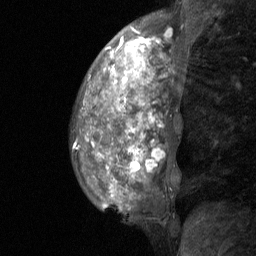
Breast MRI (dynamic contrast-enhanced), one sagittal slice. Slice 22 of 64 in the series (ordered by position). Dynamic contrast-enhanced study with each time point stored as its own series, time point 2 of 3 at this slice position (early post-contrast, ordered by acquisition time). 1.5 T. TE 4.8 ms, TR 27 ms. 256 × 256 image matrix, field of view 180 × 180 mm. Female patient, age 36 years. From the clinical record (not read from this slice): setting: breast cancer imaged before/during neoadjuvant chemotherapy; receptor status: HR-positive, HER2-negative.
Annotated regions visible in this slice (semi-automatic segmentation, software-assisted and operator-edited):
- analysis volume of interest (the breast-tissue region the enhancement analysis was run in; not a lesion): bounding box [x1, y1, x2, y2] px = [70, 12, 211, 232]
- tumour enhancement mask (voxels above the 90 % enhancement threshold inside the analysis volume of interest): [87, 29, 170, 182]